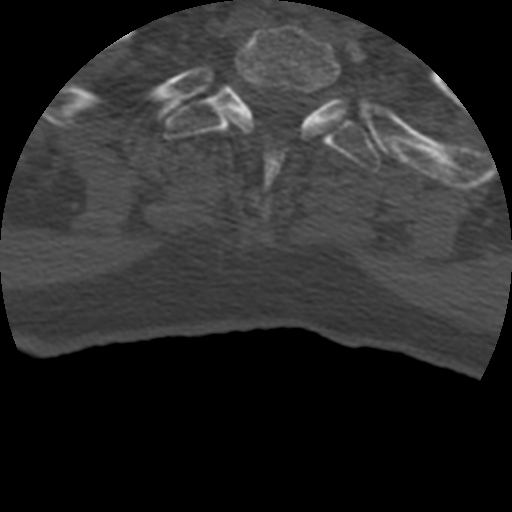
CT including the spine, one axial slice. Position 375 of 399 along the scan axis. Reconstruction kernel STANDARD. 120 kVp. Bone window (W 1800 / L 400 HU). 512 × 512 image matrix, field of view 160 × 160 mm. Patient age 69 years. From the clinical record (not read from this slice): primary cancer: prostate.
Annotated regions visible in this slice (semi-automatic segmentation, software-assisted and operator-edited):
- T1 vertebra: bounding box [x1, y1, x2, y2] px = [231, 26, 351, 183]
- T2 vertebra: [165, 84, 381, 172]